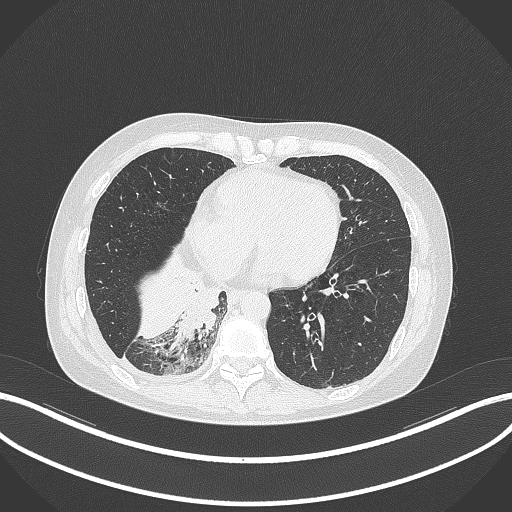
Chest CT, one axial slice; position 101 of 329 along the scan axis; reconstruction kernel B70f; 120 kVp; lung window (W 1500 / L -600 HU); 1 mm slice thickness; 512 × 512 image matrix, field of view 400 × 400 mm. Female patient, age 63 years. From the clinical record (not read from this slice): clinical TNM (as recorded): T1c N0 M0.
Outlined on this slice (bounding box drawn by a radiologist):
- lung tumour (recorded histology: adenocarcinoma): bounding box (x1, y1, x2, y2) in pixels: (176, 285, 224, 348)